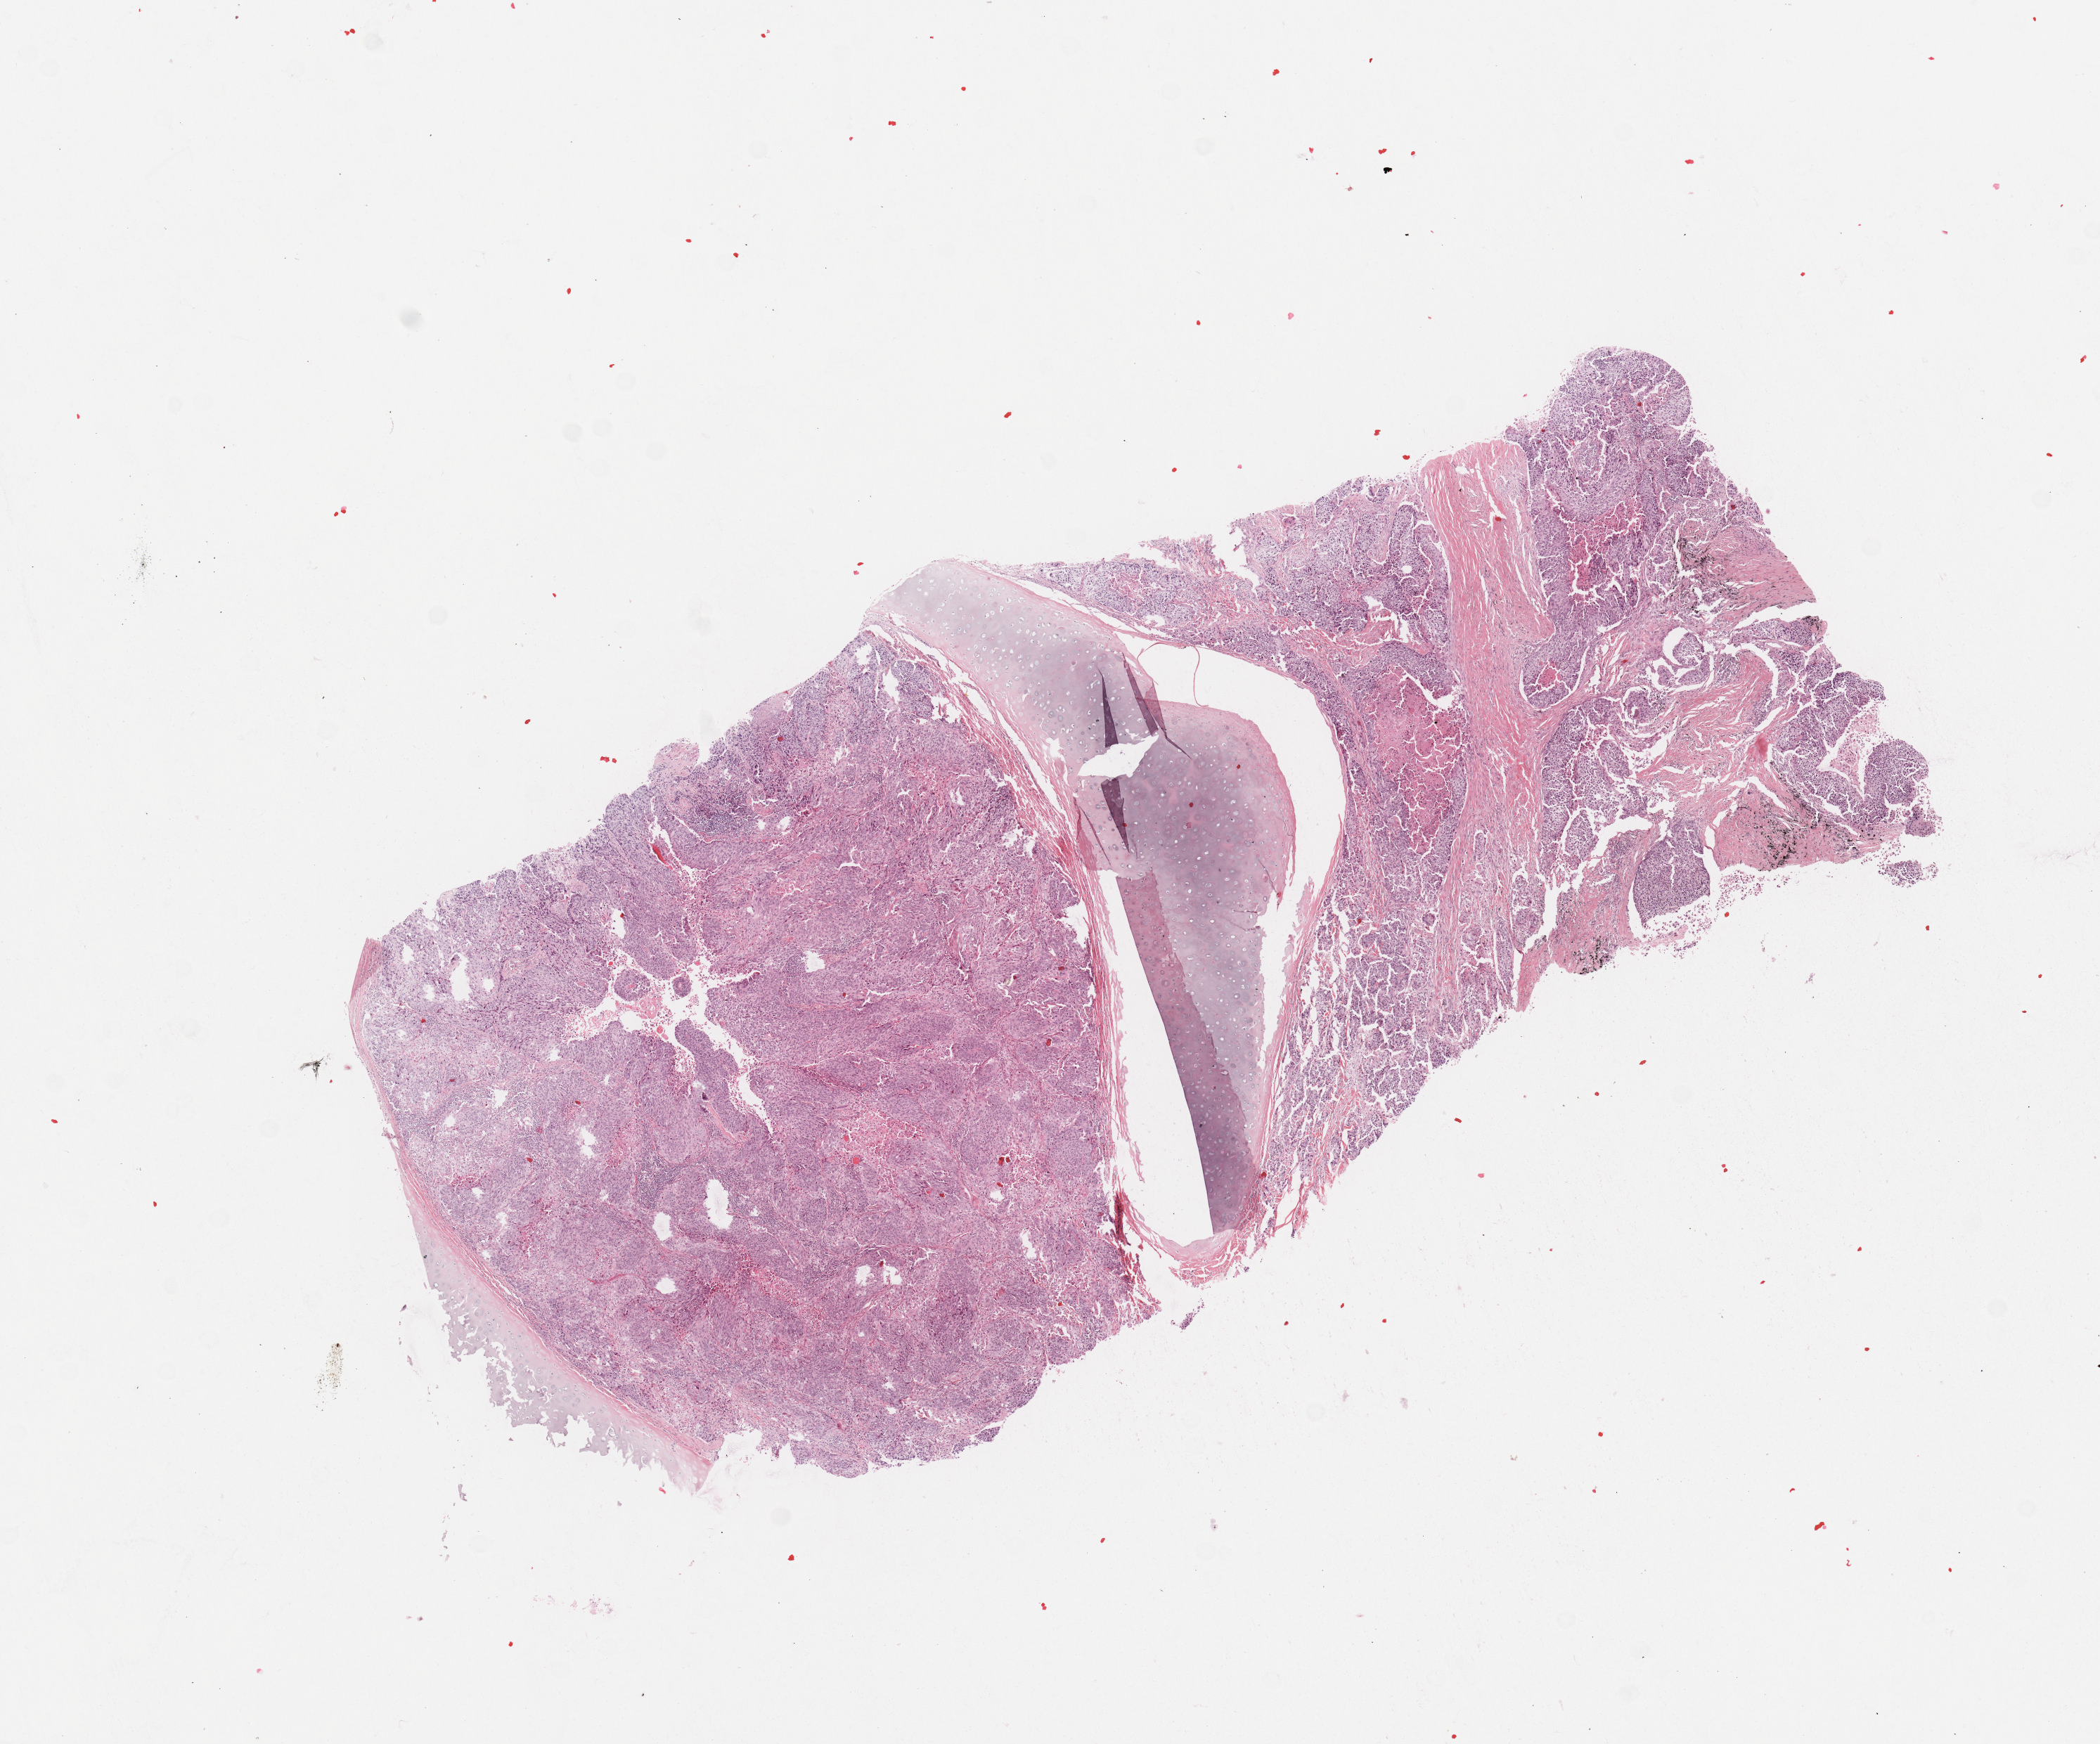
Digitized Hematoxylin and eosin (H&E) stained tissue section (whole slide), low-resolution overview of the scanned area, about 11.8 x 9.8 mm. Lung, tumour tissue. 68-year-old male patient. Histologic grade: G3 (poorly differentiated).
* diagnosis: Squamous cell carcinoma, NOS
* primary tumour site (as recorded): left upper lobe
* AJCC pathologic stage: IIB